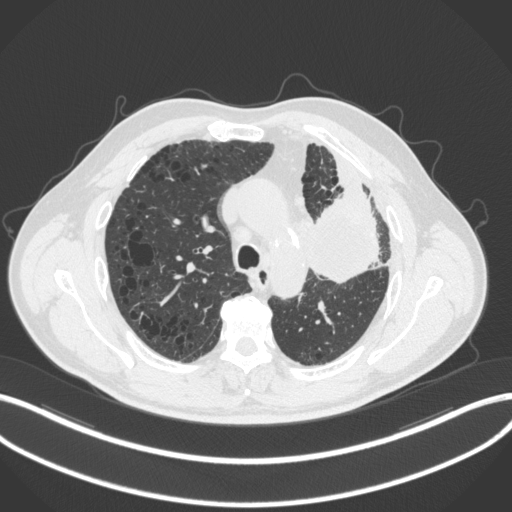
Chest CT, one axial slice; position 207 of 286 along the scan axis; 120 kVp; lung window (W 1500 / L -600 HU); 512 × 512 image matrix, field of view 400 × 400 mm. Patient: male, 68 years. Case-level facts recorded for this patient, not image findings: clinical TNM (as recorded): T3 N3 M1.
Structures marked on this image (rectangle marked by the reading radiologist):
- lung tumour (recorded histology: adenocarcinoma): box from (x=301, y=181) to (x=386, y=285) px